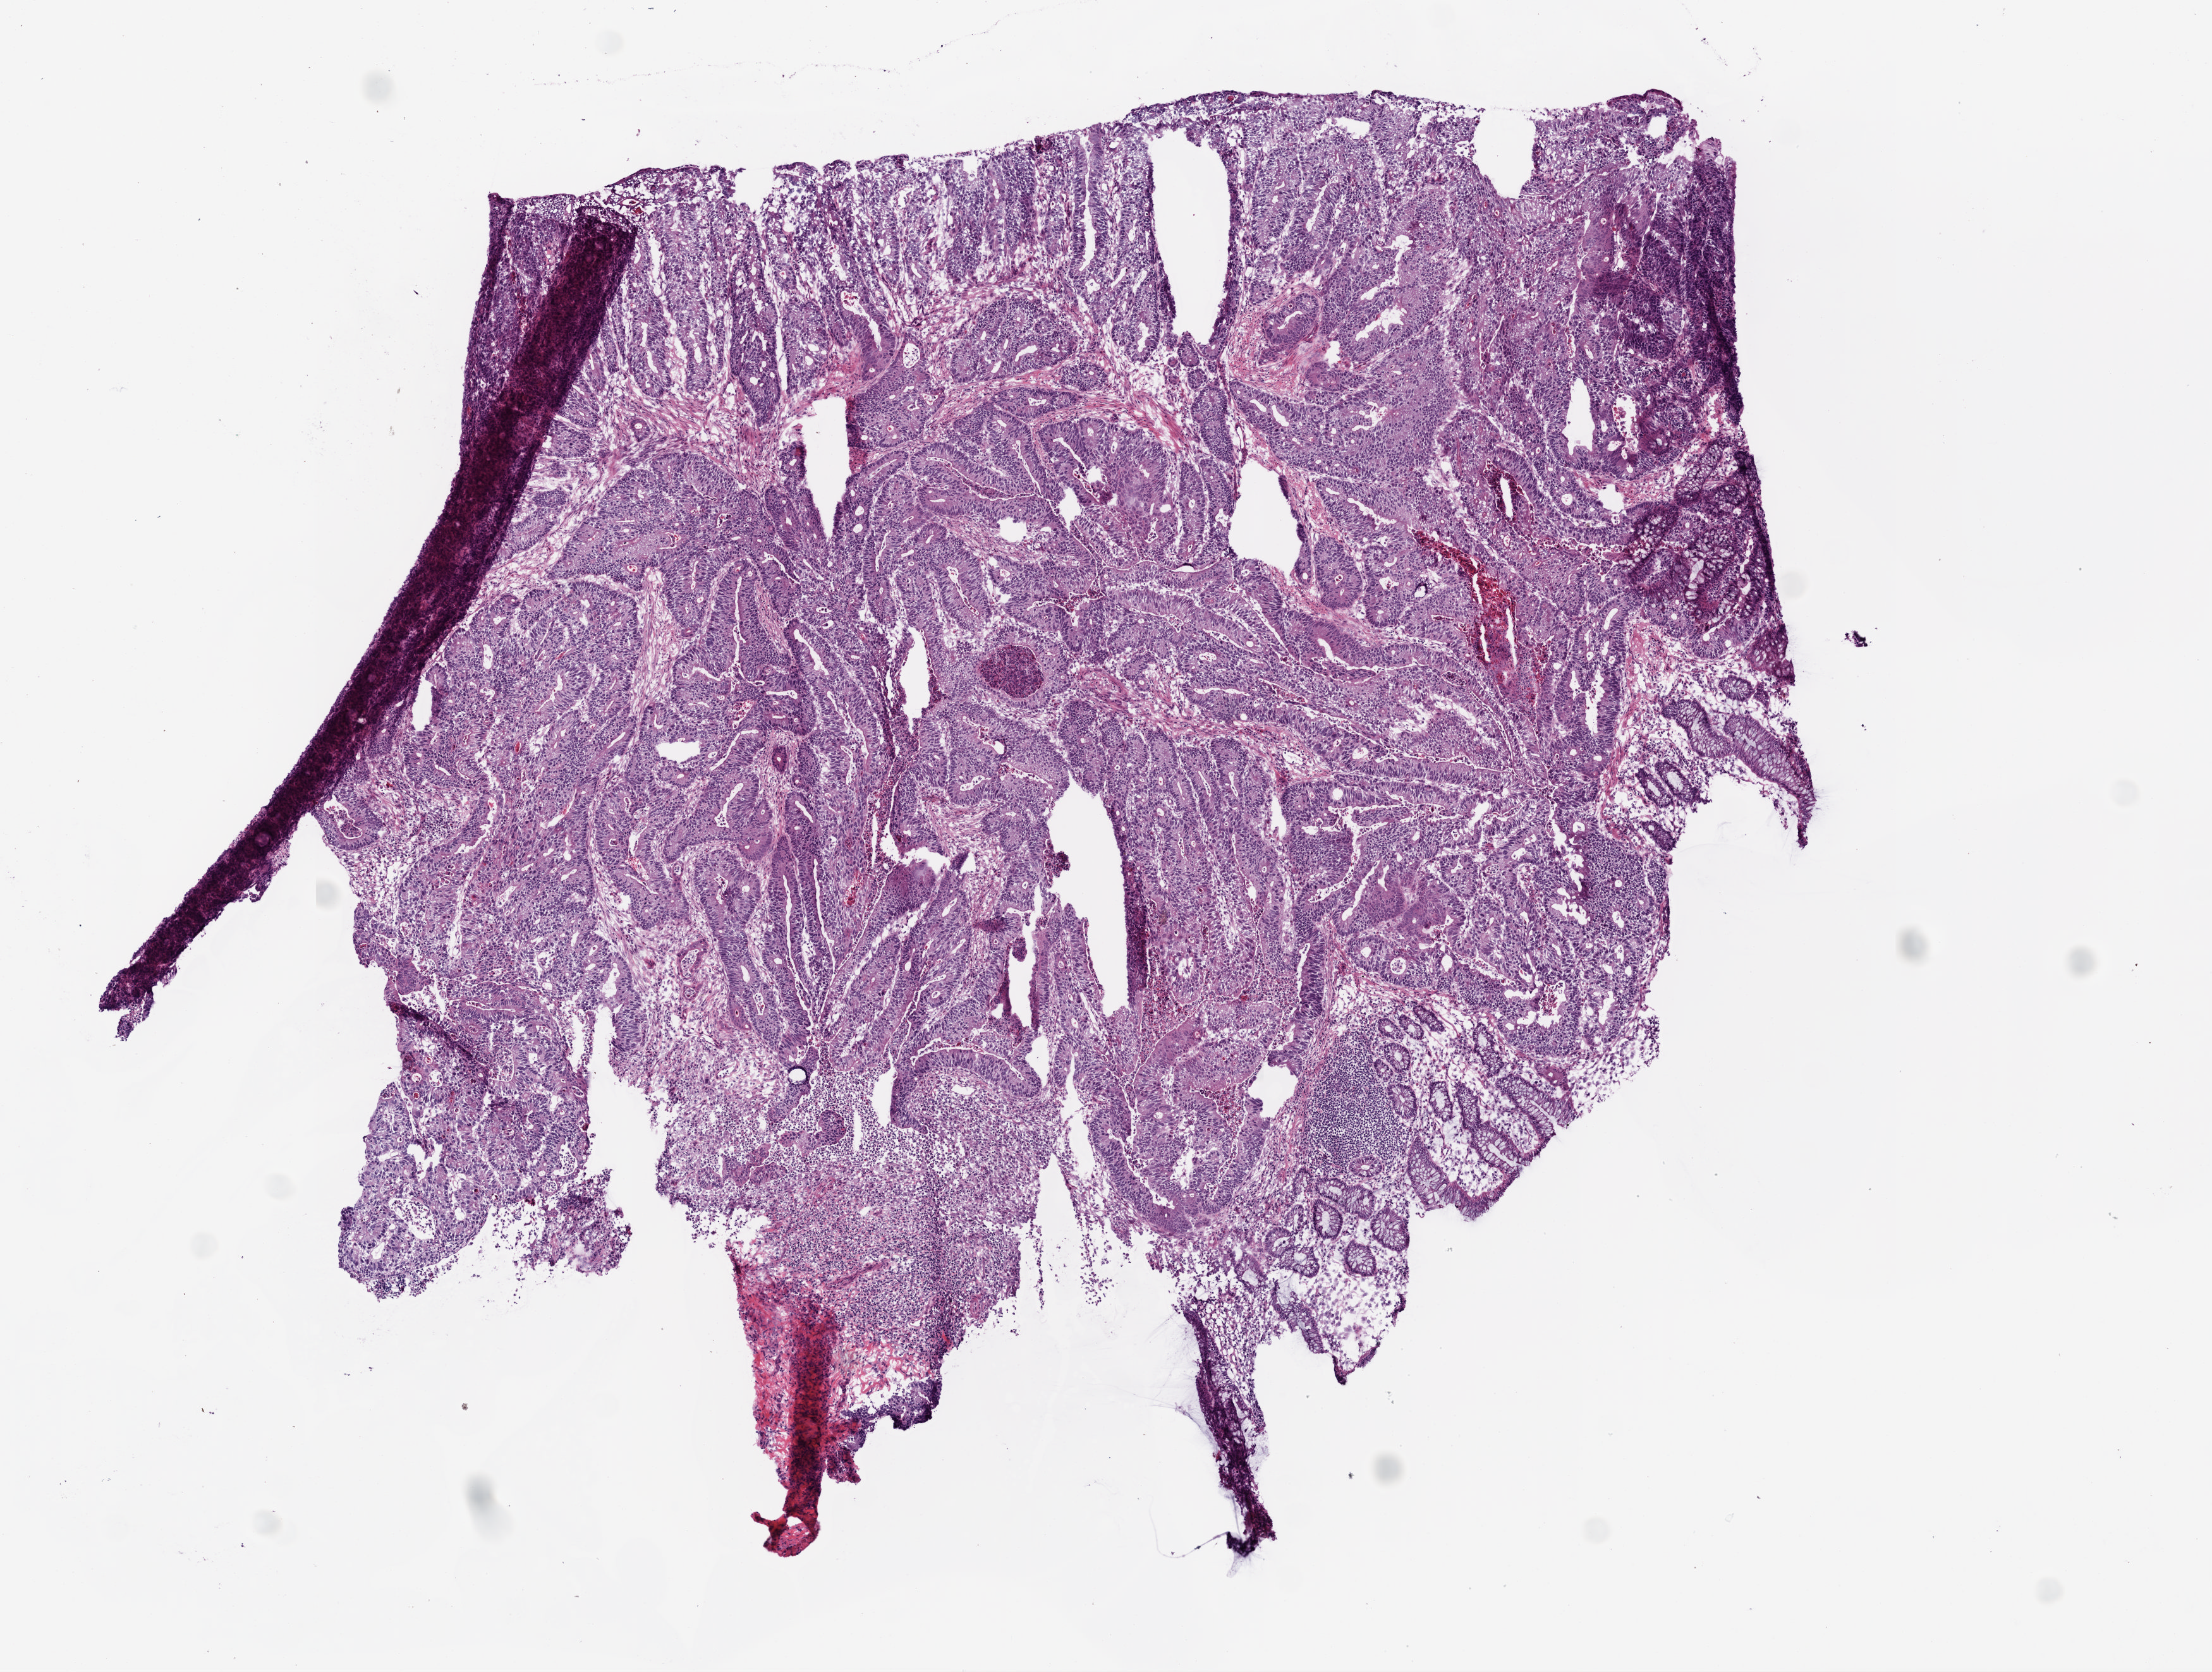
Whole-slide histology image, Hematoxylin and eosin (H&E) stained, a low-resolution overview of the entire scanned area, about 7.0 x 5.3 mm (slide scanned at 20x); frozen section from the top of the tissue portion; sample: primary tumour, colon. Patient: female, age at initial diagnosis 80 years. Slide review estimates, as recorded: tumour cells 80%, tumour nuclei 90%, normal cells 10%, stromal cells 10%, necrosis 0%. Inflammatory infiltration, as recorded: lymphocyte infiltration 1%.
Lymph nodes positive (case pathology): 4 of 15 examined. AJCC pathologic stage: IV. Pathologic diagnosis: Adenocarcinoma, NOS.